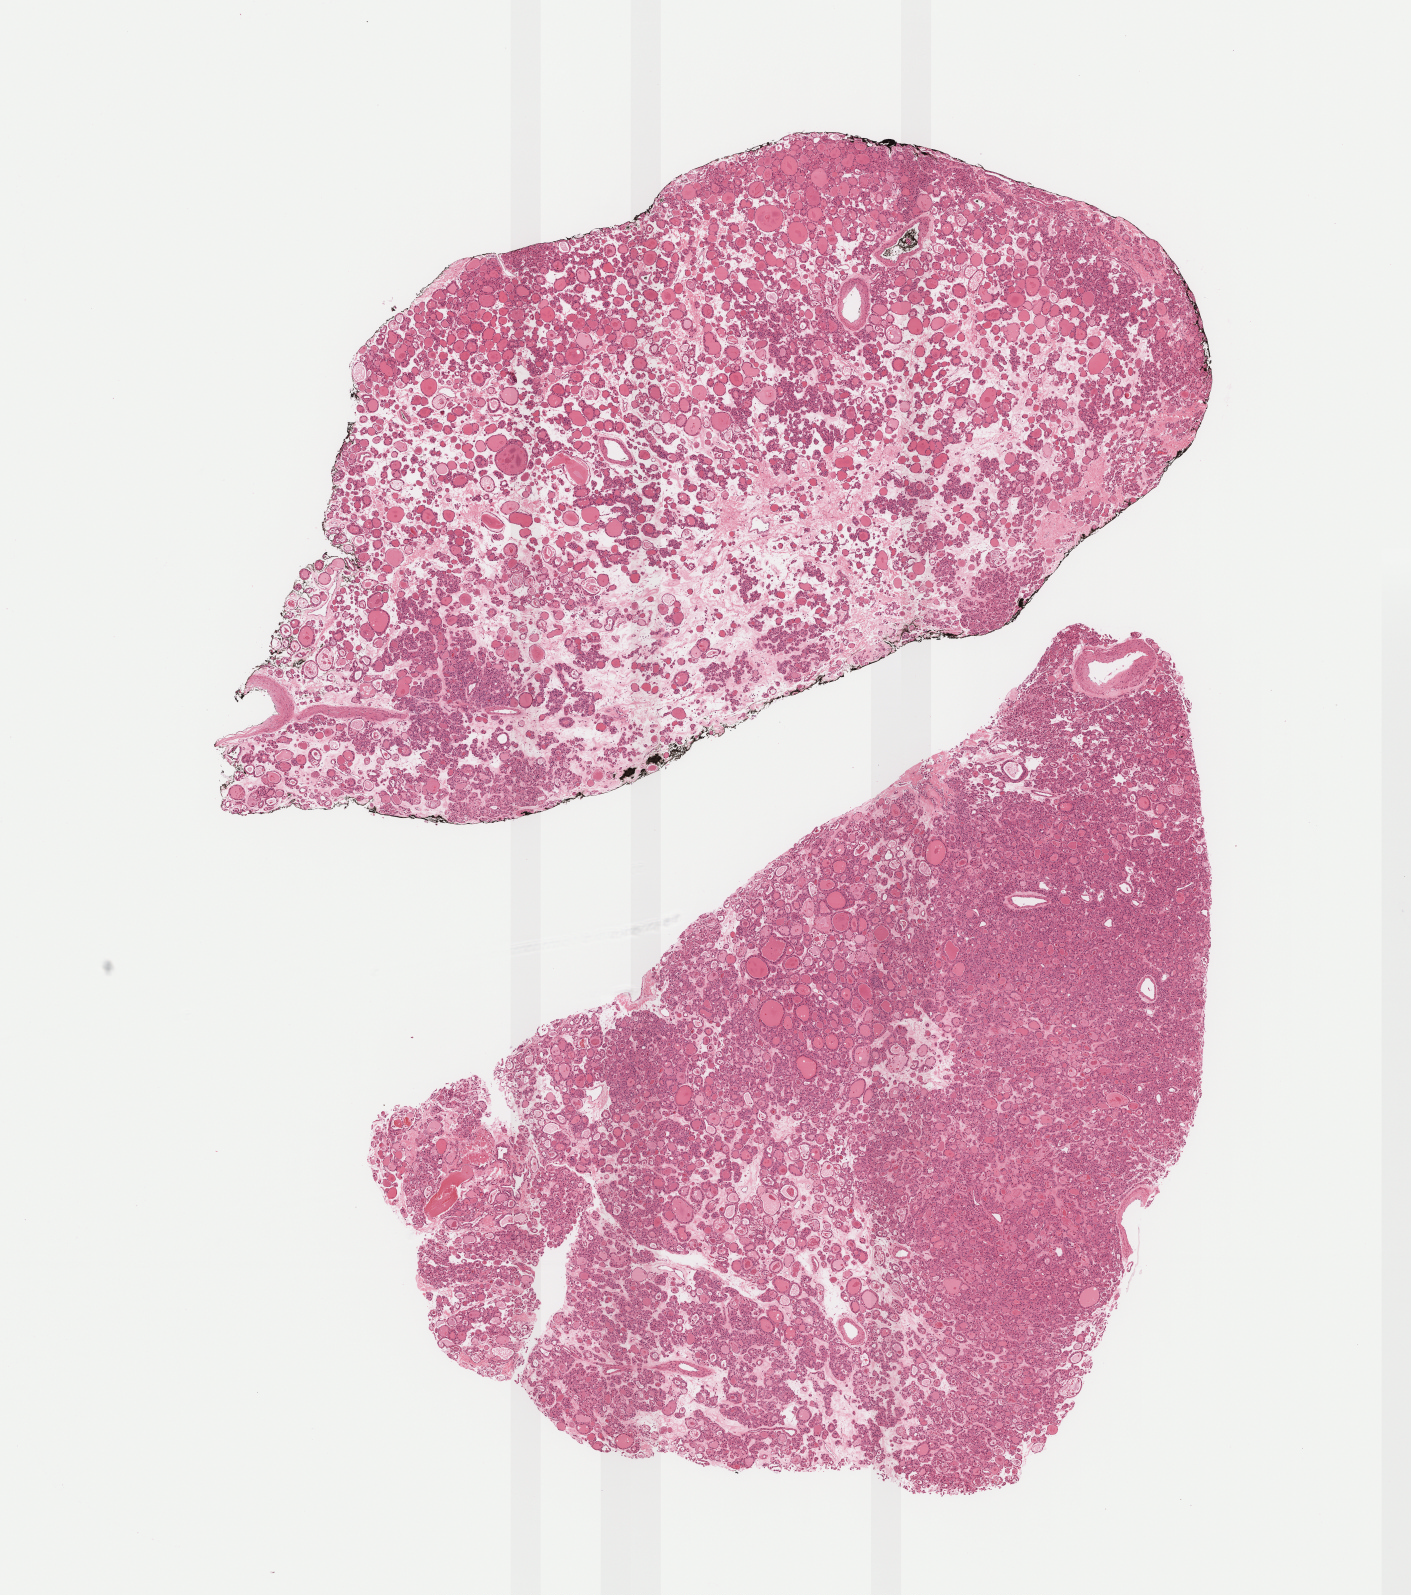
Whole-slide histology image, H&E-stained, a low-resolution overview of the entire scanned area, about 11.4 x 12.9 mm. Formalin-fixed paraffin-embedded (FFPE) diagnostic section. Sample: primary tumour, thyroid. Female, age 77 years at initial diagnosis.
AJCC pathologic stage: II (7th edition). Pathologic diagnosis: Papillary carcinoma, follicular variant (thyroid gland).